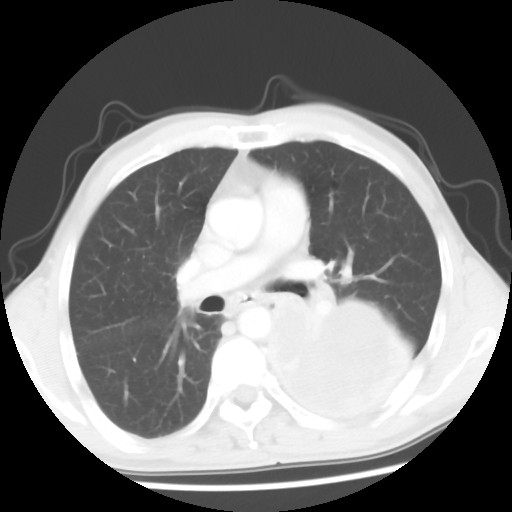
Chest CT, one axial slice. Position 33 of 56 along the scan axis. Reconstruction kernel STANDARD. 120 kVp. Lung window (W 1500 / L -600 HU). 5 mm slice thickness. 512 × 512 image matrix. Male patient, age 60 years. From the clinical record (not read from this slice): clinical TNM (as recorded): T4 N0 M0.
Outlined on this slice (bounding box drawn by a radiologist):
- lung tumour (recorded histology: squamous cell carcinoma): bounding box <261,283,430,426> (left, top, right, bottom; pixels)